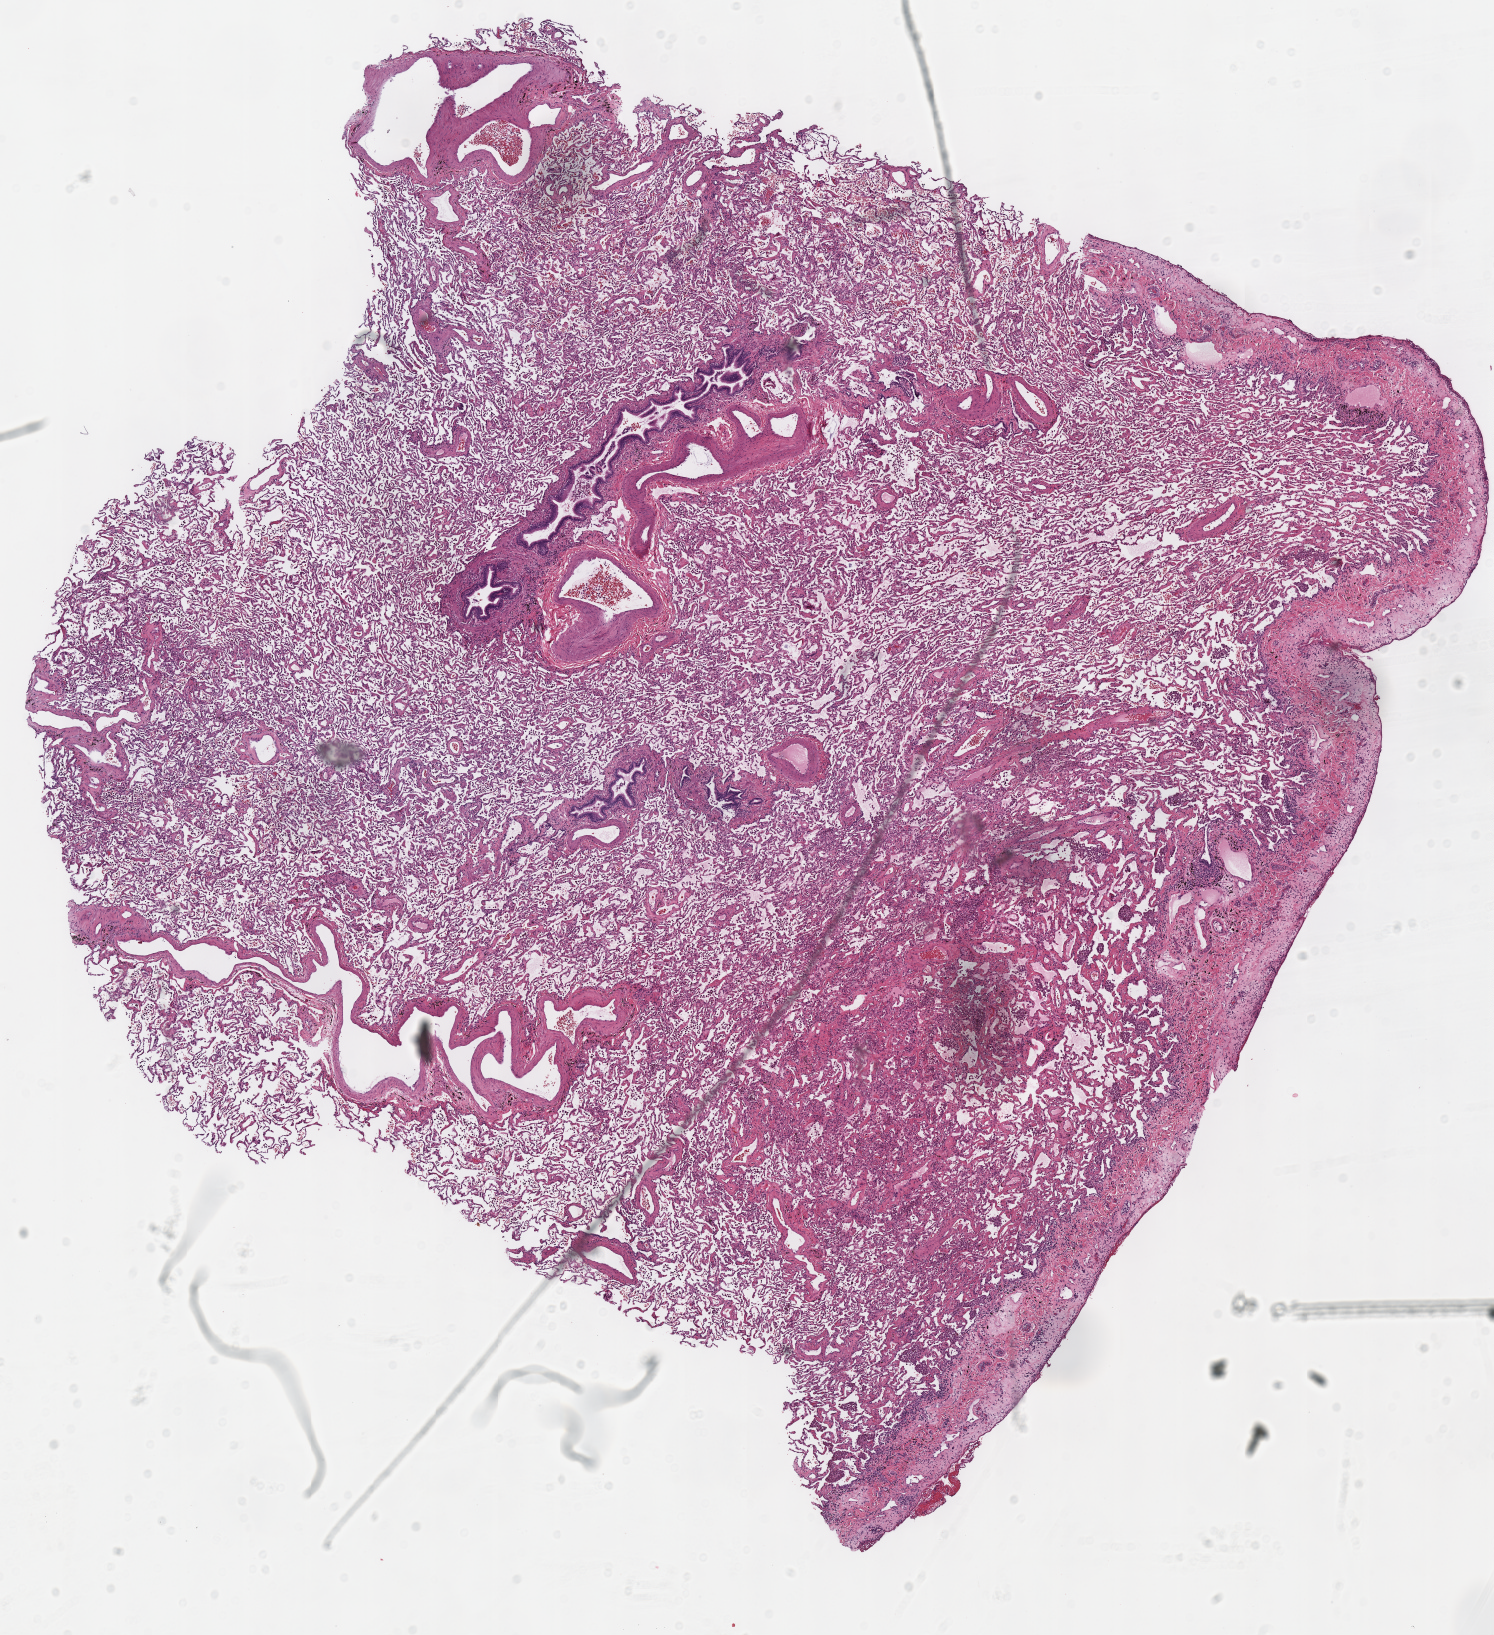
Digitized Hematoxylin and eosin (H&E) stained tissue section (whole slide) — shown as a low-resolution overview of the whole scanned area (about 11.7 x 12.9 mm); frozen section from the top of the tissue portion; solid tissue normal (non-tumour tissue) sample from the lung. Female patient; age at initial diagnosis 49 years.
This section: solid tissue normal (non-tumour) sample from the same patient. Patient diagnosis: Adenocarcinoma, NOS (lower lobe, lung).